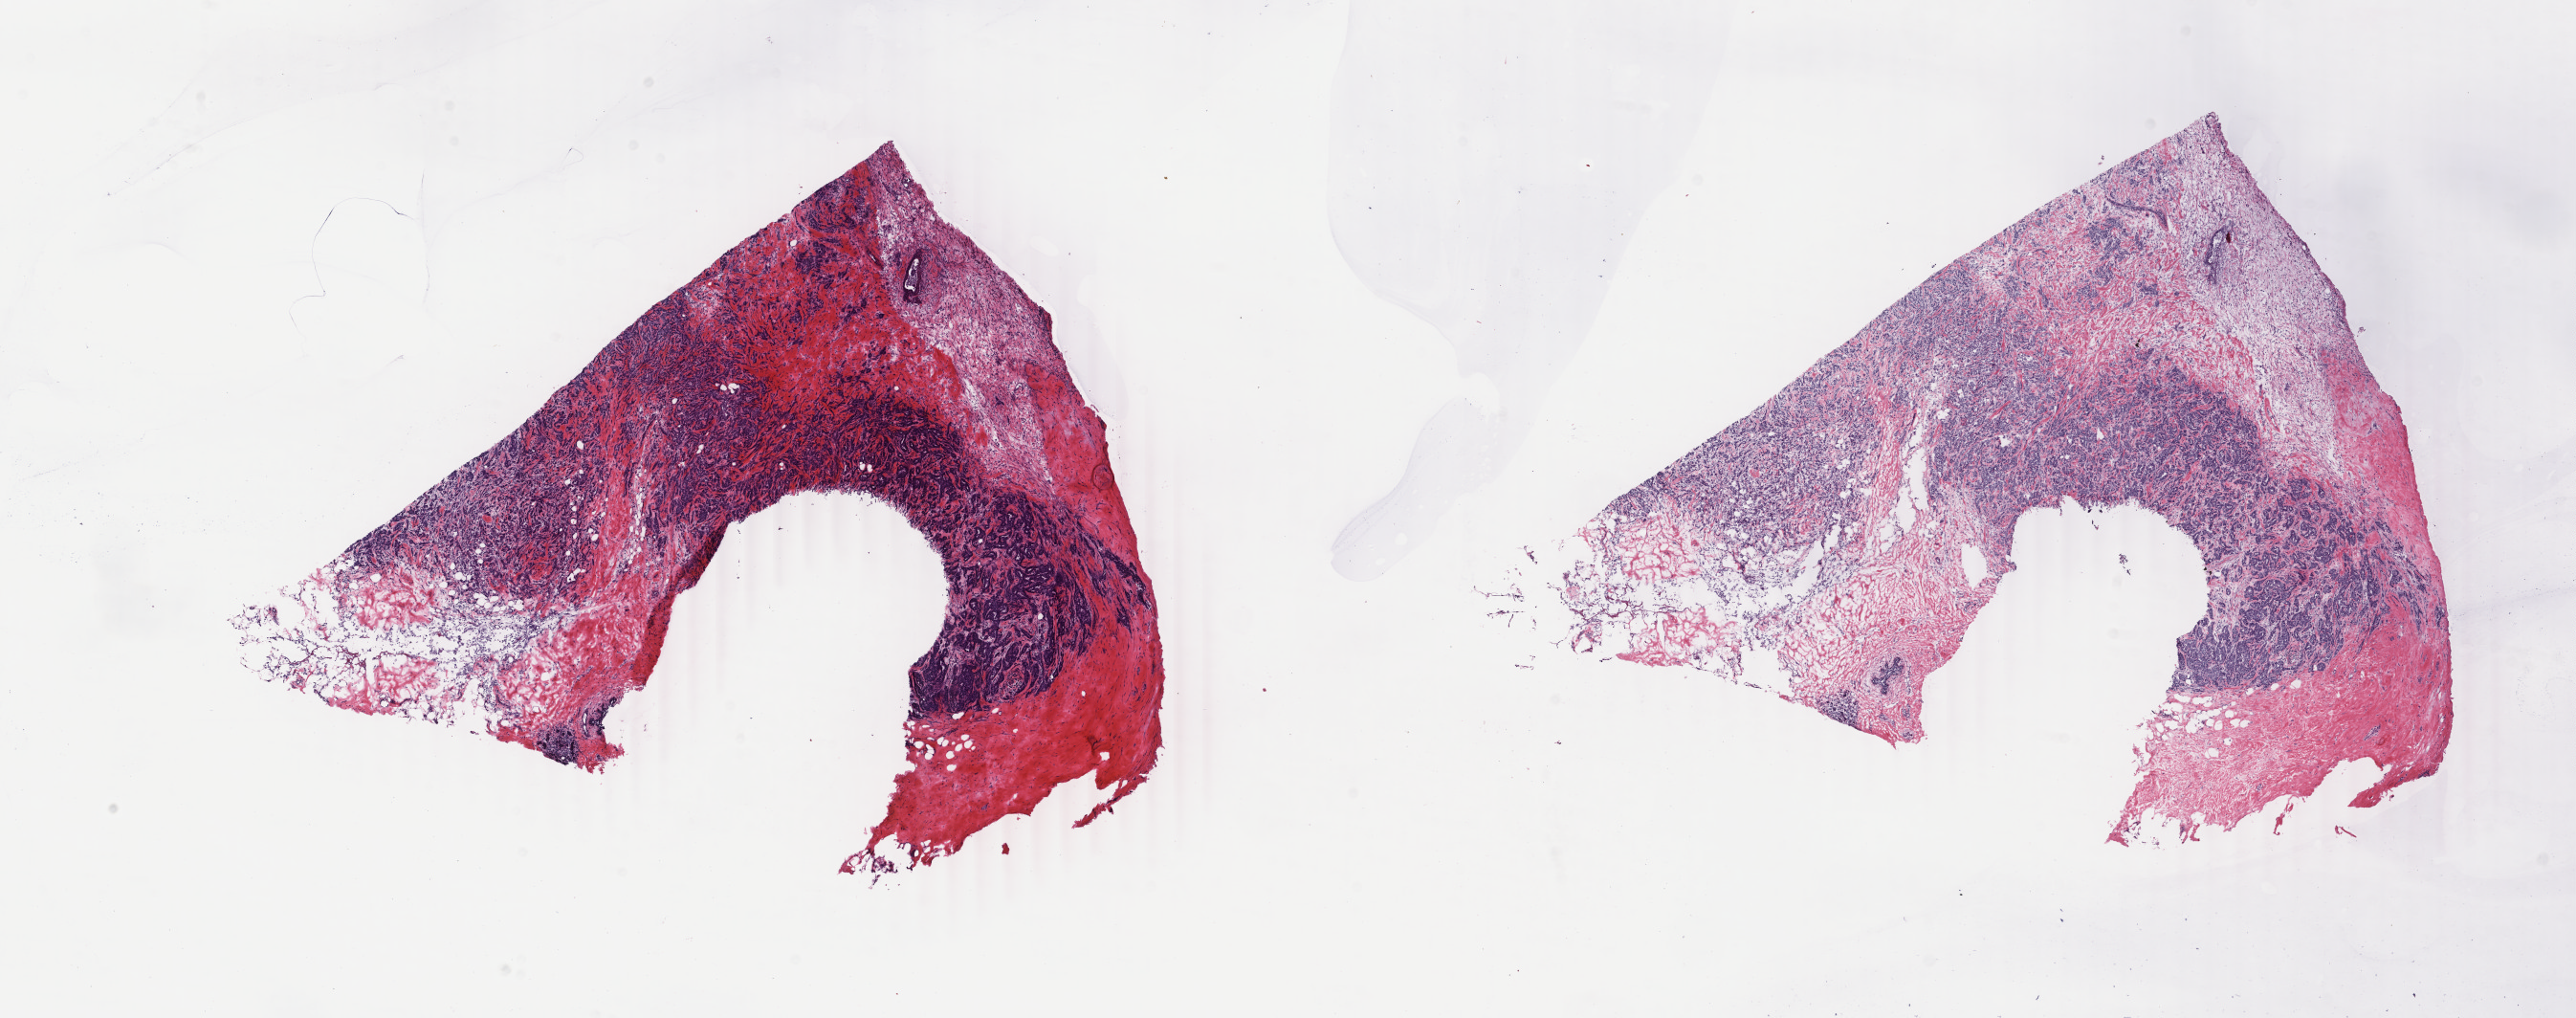
H&E-stained whole-slide image, low-resolution overview of the scanned area, about 21.4 x 8.5 mm. Frozen section from the top of the tissue portion. Sample: primary tumour, breast. Patient: female, age at initial diagnosis 43 years. Composition of this section per pathologist review: tumour cells 60%, tumour nuclei 70%.
Diagnosis: Infiltrating duct carcinoma, NOS.